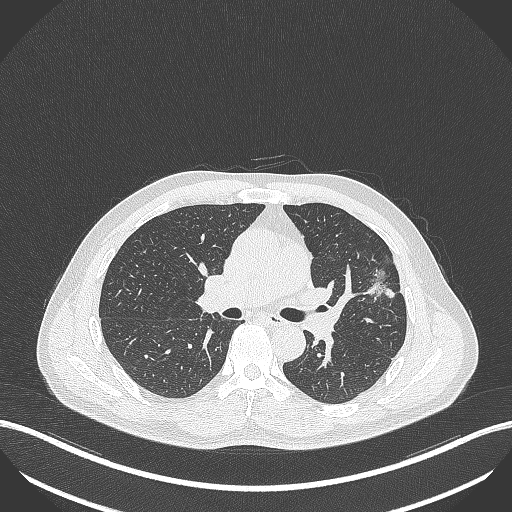
Chest CT, one axial slice; position 232 of 418 along the scan axis; 120 kVp; lung window (W 1500 / L -600 HU); 1 mm slice thickness; 512 × 512 image matrix. Male patient, age 55 years. Case-level facts recorded for this patient, not image findings: clinical TNM (as recorded): T1c N0 M0; histopathological grade: G2-3.
Structures marked on this image (rectangle marked by the reading radiologist):
- lung tumour (recorded histology: adenocarcinoma): bounding box (x1, y1, x2, y2) in pixels: (364, 268, 401, 302)